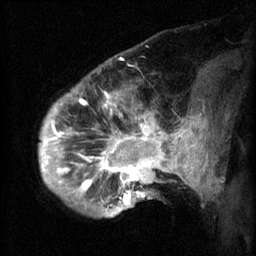
Breast MRI (dynamic contrast-enhanced), one sagittal slice. Slice 15 of 60 in the series (ordered by position). 3 images stored at this slice position (order not interpretable as contrast timing). 1.5 T. TE 4.2 ms, TR 8.2 ms. 2.3 mm slice thickness. 256 × 256 image matrix, field of view 200 × 200 mm. Female patient, age 50 years.
Structures marked on this image (semi-automatically segmented with operator editing):
- analysis volume of interest (the breast-tissue region the enhancement analysis was run in; not a lesion): box from (x=50, y=64) to (x=169, y=217) px
- tumour enhancement mask (voxels above the 70 % enhancement threshold inside the analysis volume of interest): (x=50, y=94)–(x=169, y=205)